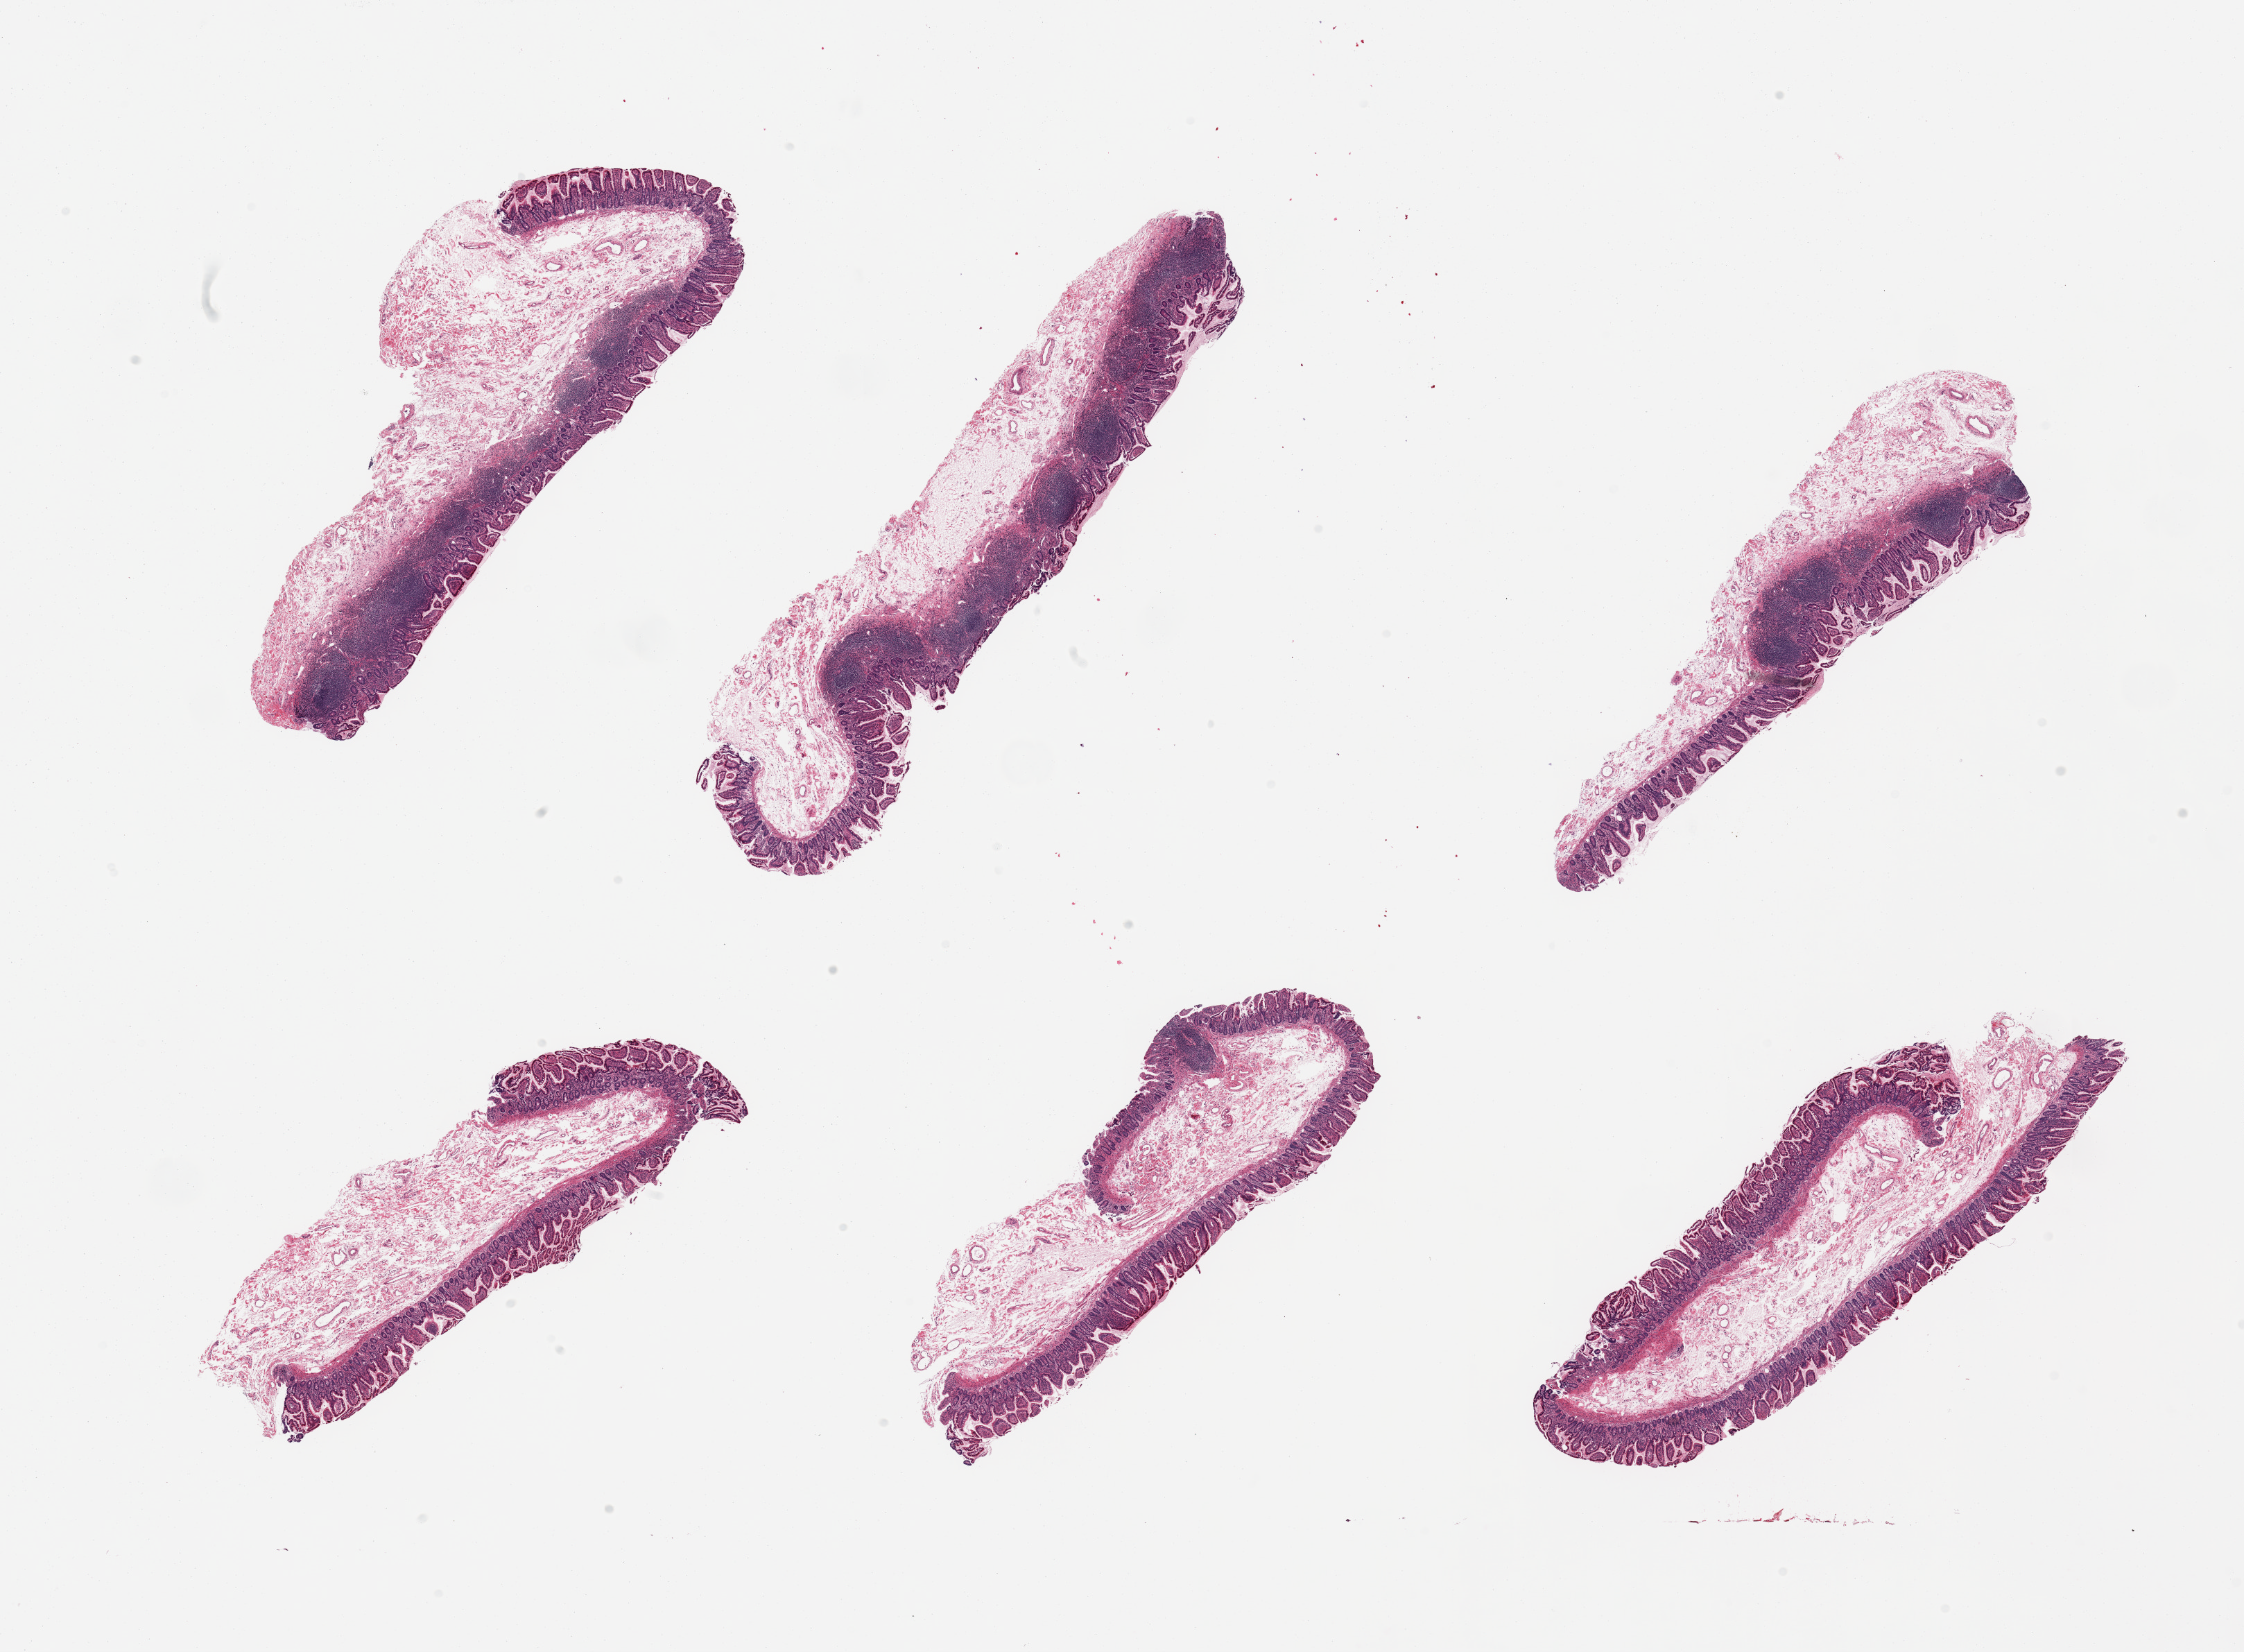
Whole-slide image, hematoxylin and eosin (H&E) stain, a low-resolution overview of the entire scanned area, about 25.6 x 18.8 mm, PAXgene-fixed, paraffin-embedded tissue, target tissue: ileum, donor tissue sample. Donor: male.
Review note (as recorded): 6 pieces; mucosa/submucosa with pronounced lymphoid component in 3 of 6.